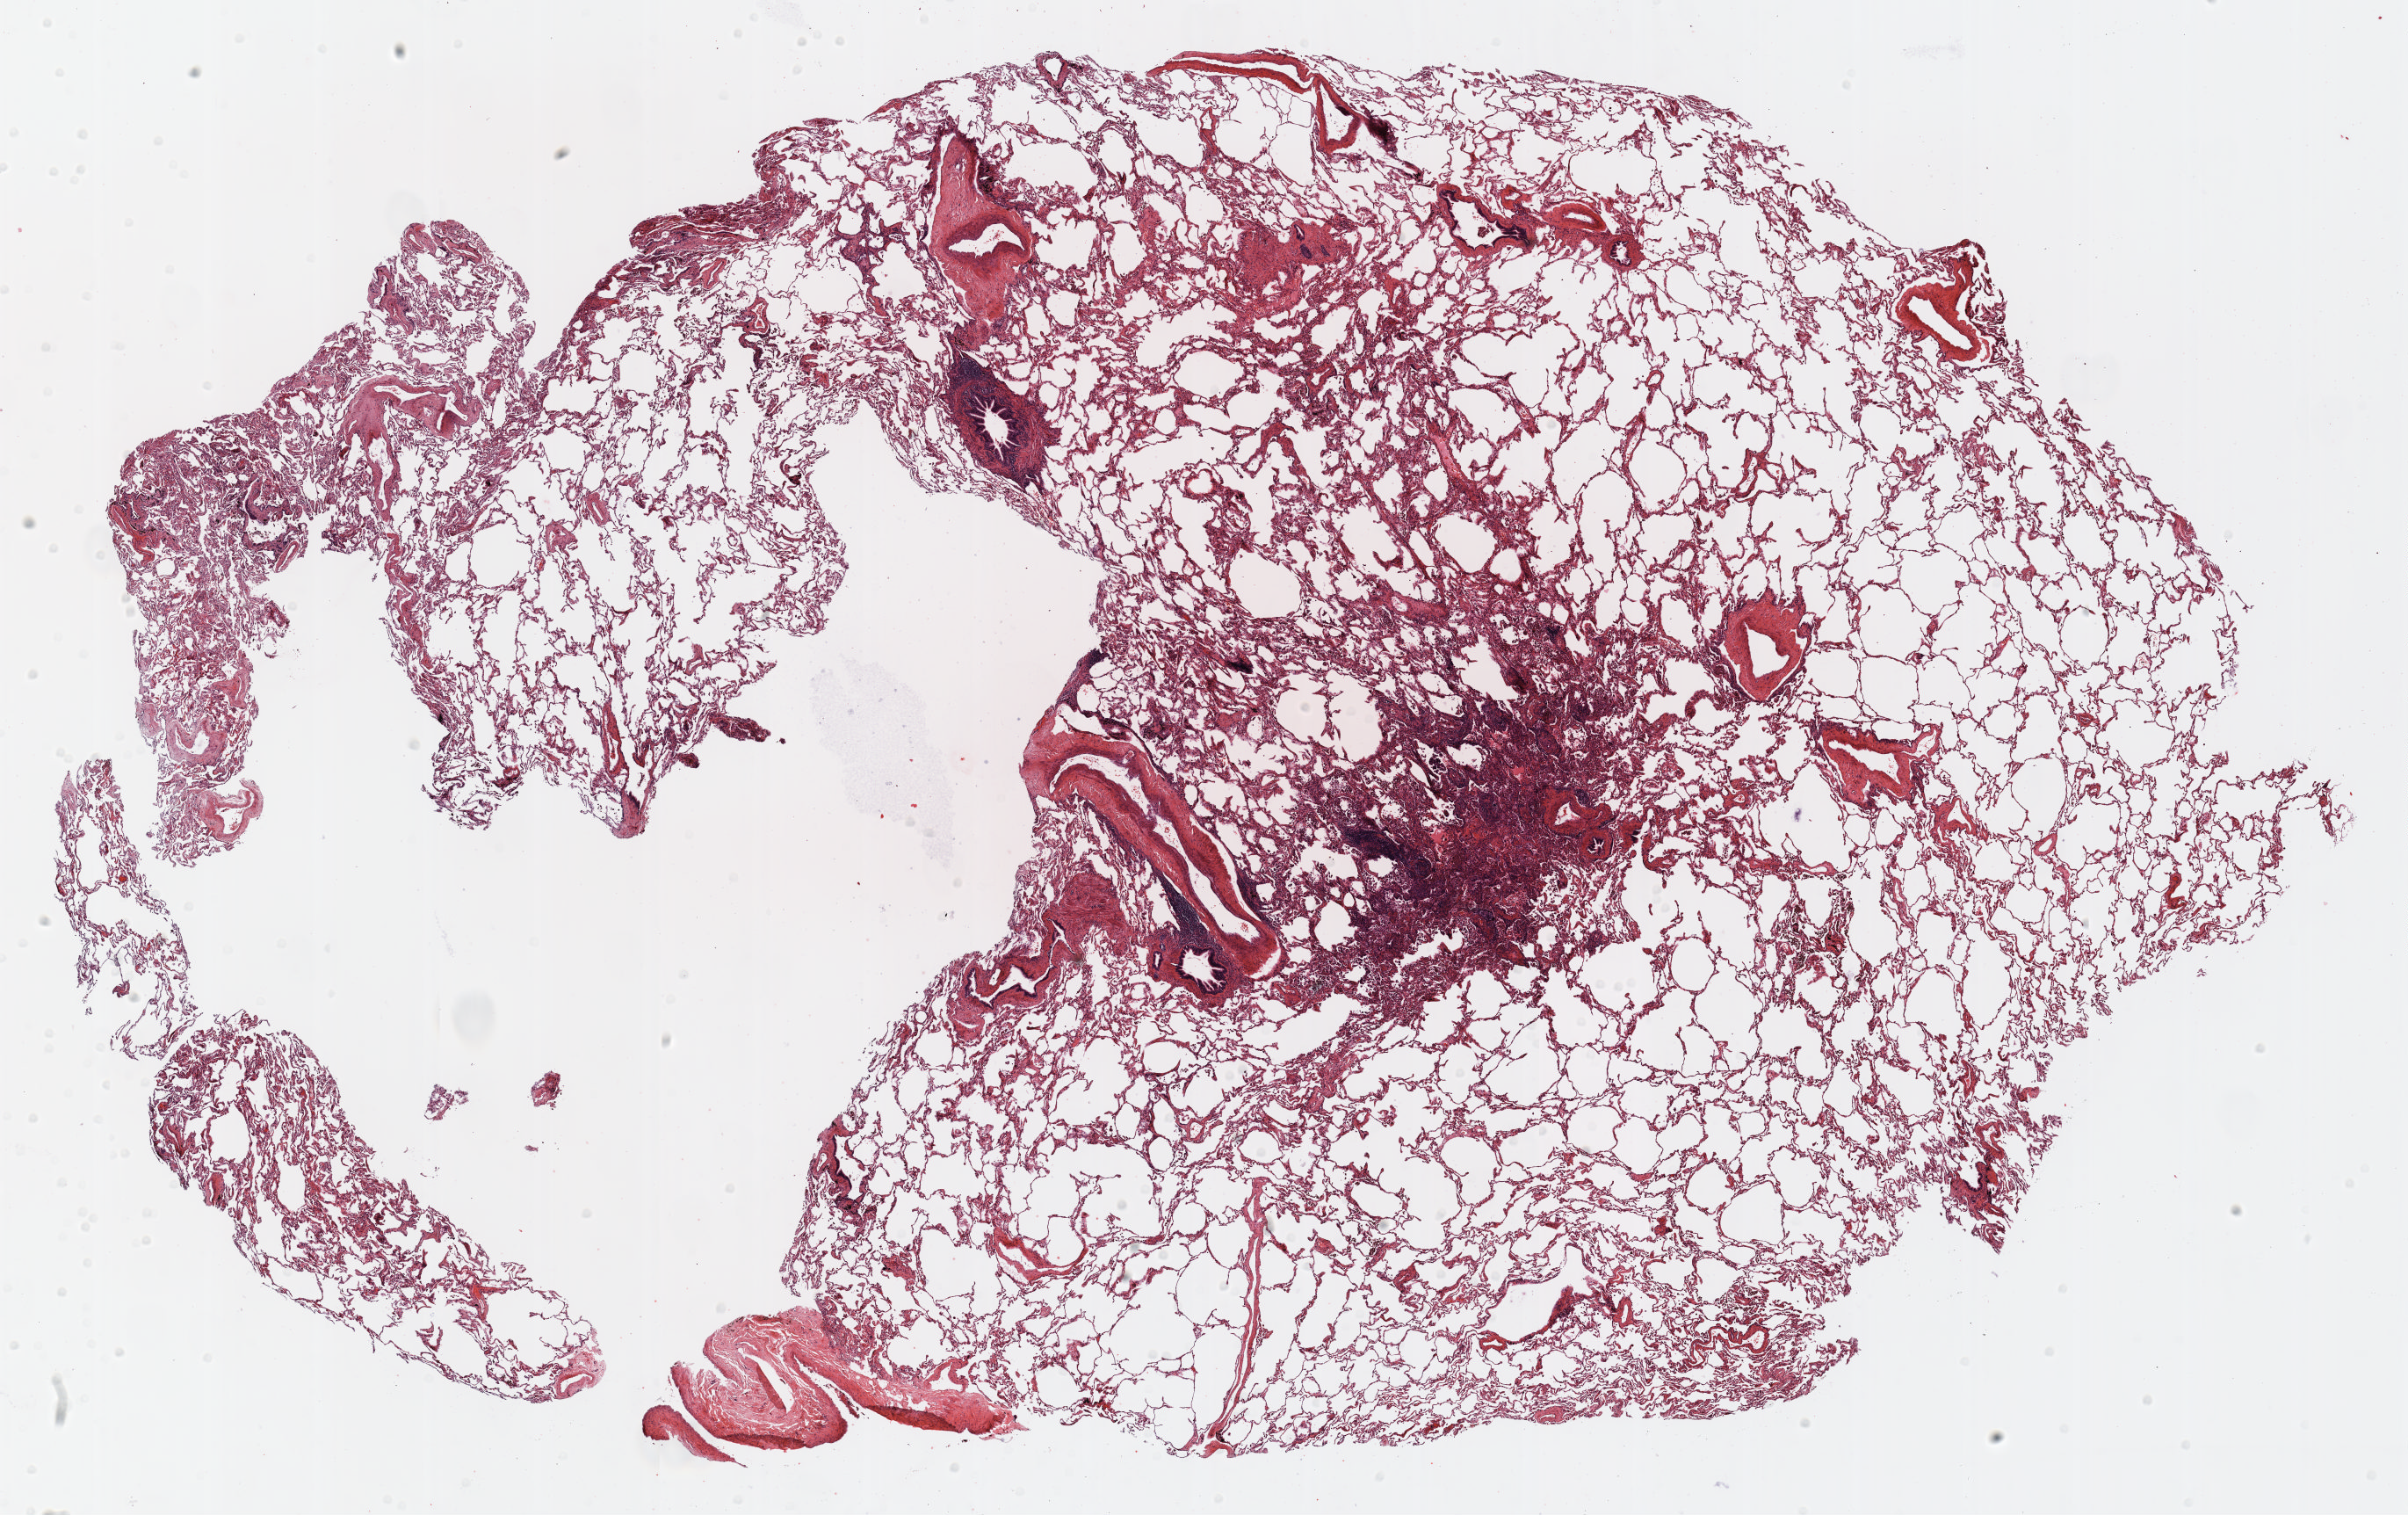
H&E whole-slide image, low-resolution overview of the scanned area, about 22.0 x 13.9 mm (acquisition: 20x scan), FFPE section, lung. Male, age 58 at enrolment. Current smoker at enrolment. Grade: poorly differentiated (G3).
Primary tumour location (clinical record): right lower lobe. Participant's lung-cancer diagnosis: Adenocarcinoma, NOS (ICD-O-3 8140/3). ICD-O-3 topography: lower lobe of lung (C34.3). Stage (AJCC 6th edition): IIIA. Tumour size (pathology): 15 mm.